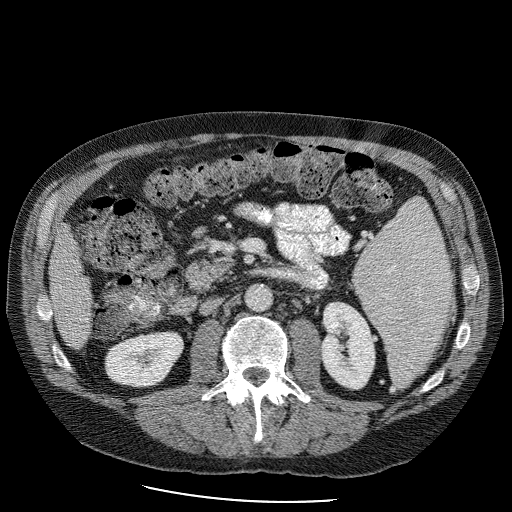
Contrast-enhanced abdominal CT (liver protocol), one axial slice. Slice 28 of 98 in the series (ordered by position). Reconstruction kernel STANDARD. Soft-tissue window (W 400 / L 40 HU). 512 × 512 image matrix, field of view 400 × 400 mm. From the clinical record (not read from this slice): diagnosis: hepatocellular carcinoma (patient treated with transarterial chemoembolisation; whether this scan precedes or follows treatment is not stated here); TNM stage (as recorded): Stage-II; Child-Pugh class: B; tumour differentiation: moderately differentiated; tumour nodularity: uninodular.
Annotated regions visible in this slice (semi-automatic segmentation, software-assisted and operator-edited):
- liver parenchyma outside the tumour (the mass and vessels are separate outlines, so this box may not span the whole liver): box from (x=48, y=218) to (x=96, y=349) px